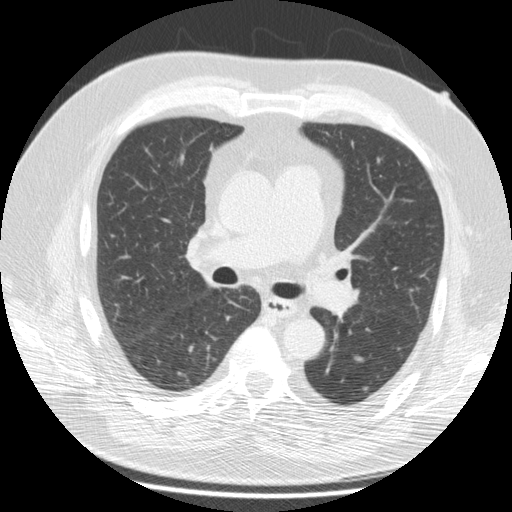
Axial slice from a low-dose chest CT screening exam; third screening round (two years after baseline); lung window (W 1500 / L -600 HU); 2.5 mm slice thickness; slice 69 of 172 in the series; 512 × 512 image matrix. Male, age 69 years at enrolment. Former smoker at enrolment.
Expert reader's lesion annotation, bounding box <351,372,383,399> (left, top, right, bottom; pixels). The screening reader recorded 2 non-calcified nodules or masses ≥4 mm on this exam (left lower lobe, left lower lobe); which of them this box marks is not recorded. Participant outcome: lung cancer diagnosed 224 days after this screen — squamous cell carcinoma, NOS, left lower lobe, moderately differentiated (G2), stage IA (AJCC 6th edition), 14 mm at pathology.